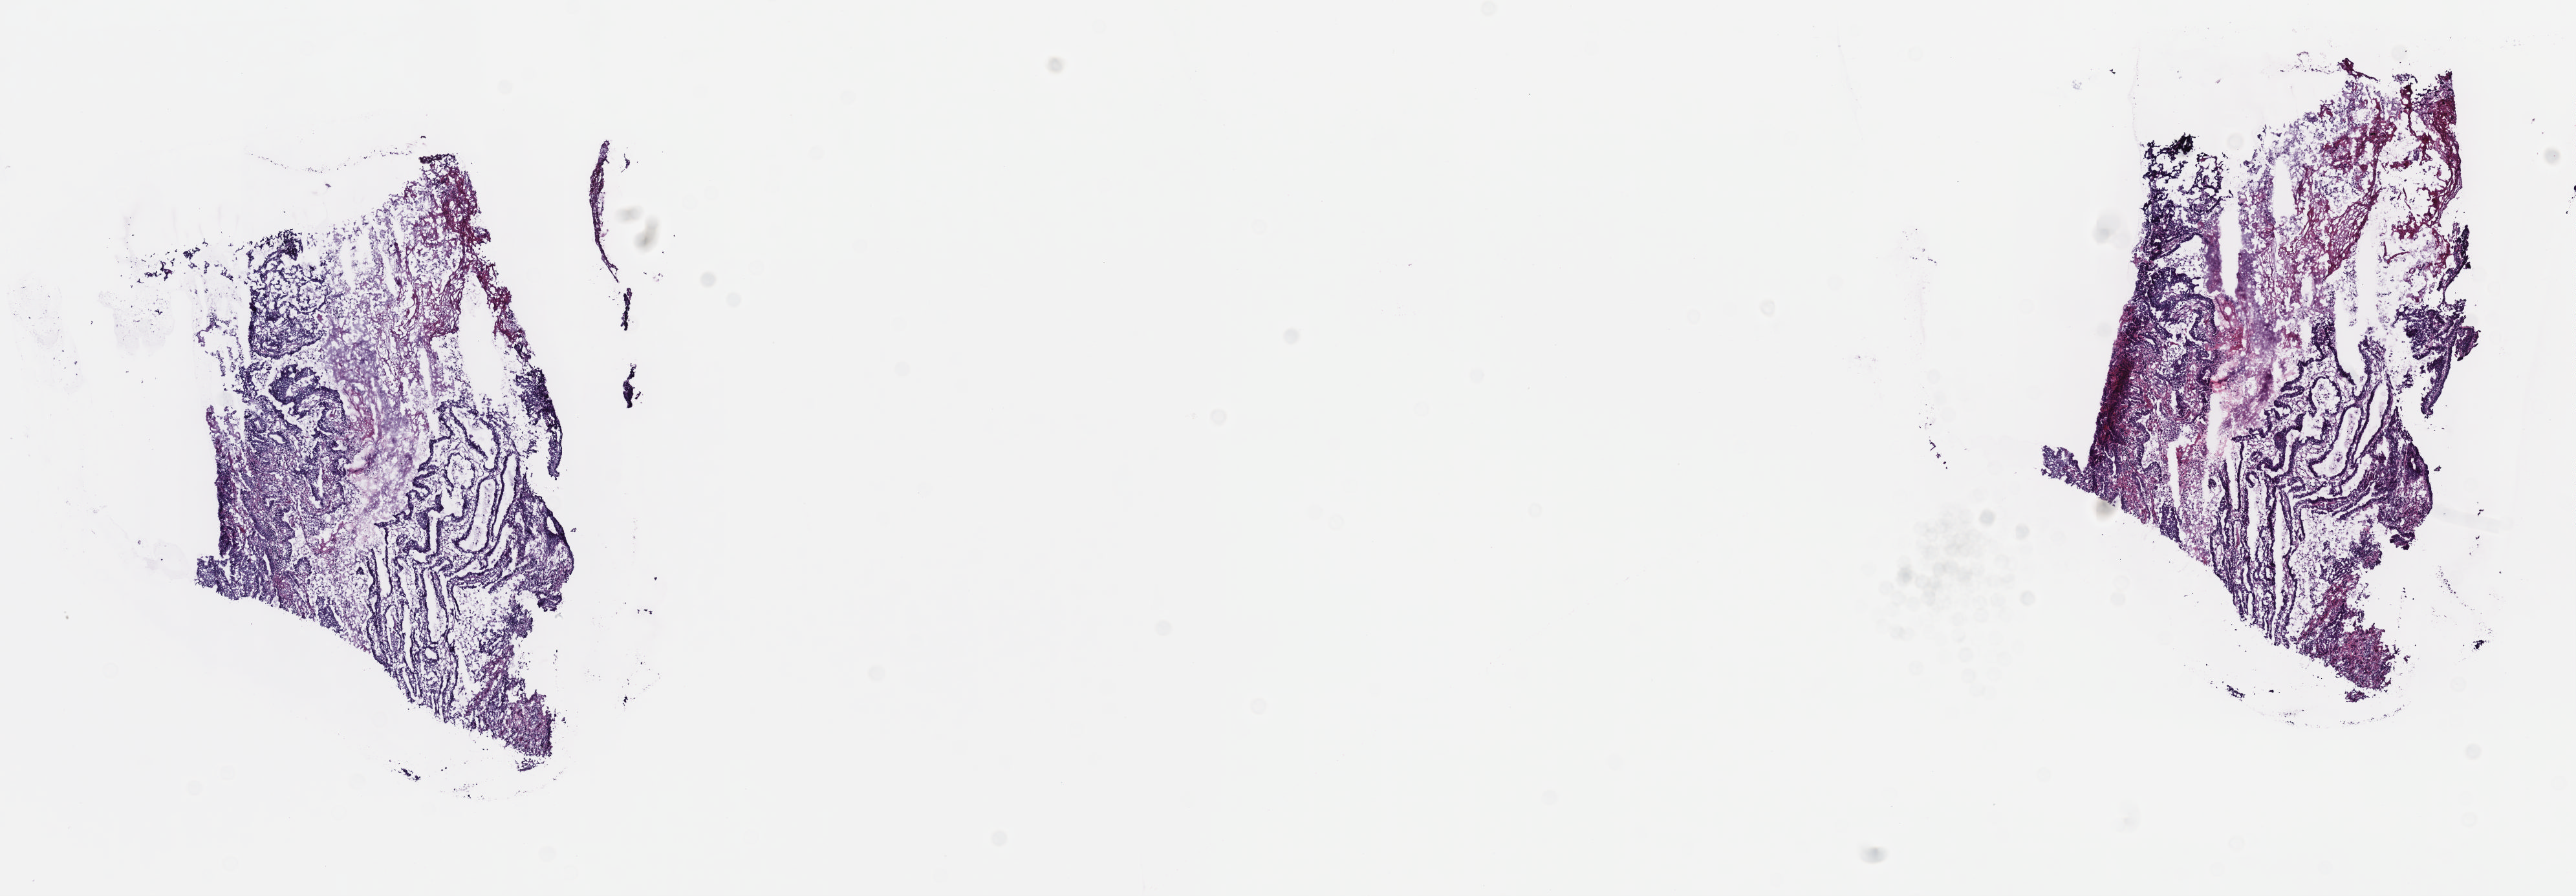
Digitized Hematoxylin and eosin (H&E) stained tissue section (whole slide) — shown as a low-resolution overview of the whole scanned area (about 16.1 x 5.6 mm, slide scanned at 40x); frozen section; stomach, primary tumour sample. Male patient; age at initial diagnosis 30 years. Histologic grade: G2 (moderately differentiated). Slide review estimates, as recorded: tumour cells 100%, tumour nuclei 65%, normal cells 0%, stromal cells 0%, necrosis 0%. Inflammatory infiltration, as recorded: lymphocyte infiltration 3%, monocyte infiltration 3%, neutrophil infiltration 0%.
AJCC pathologic stage: IIIA (6th edition). Lymph nodes positive (case pathology): 5 of 25 examined. Pathologic diagnosis: Adenocarcinoma, intestinal type (body of stomach).